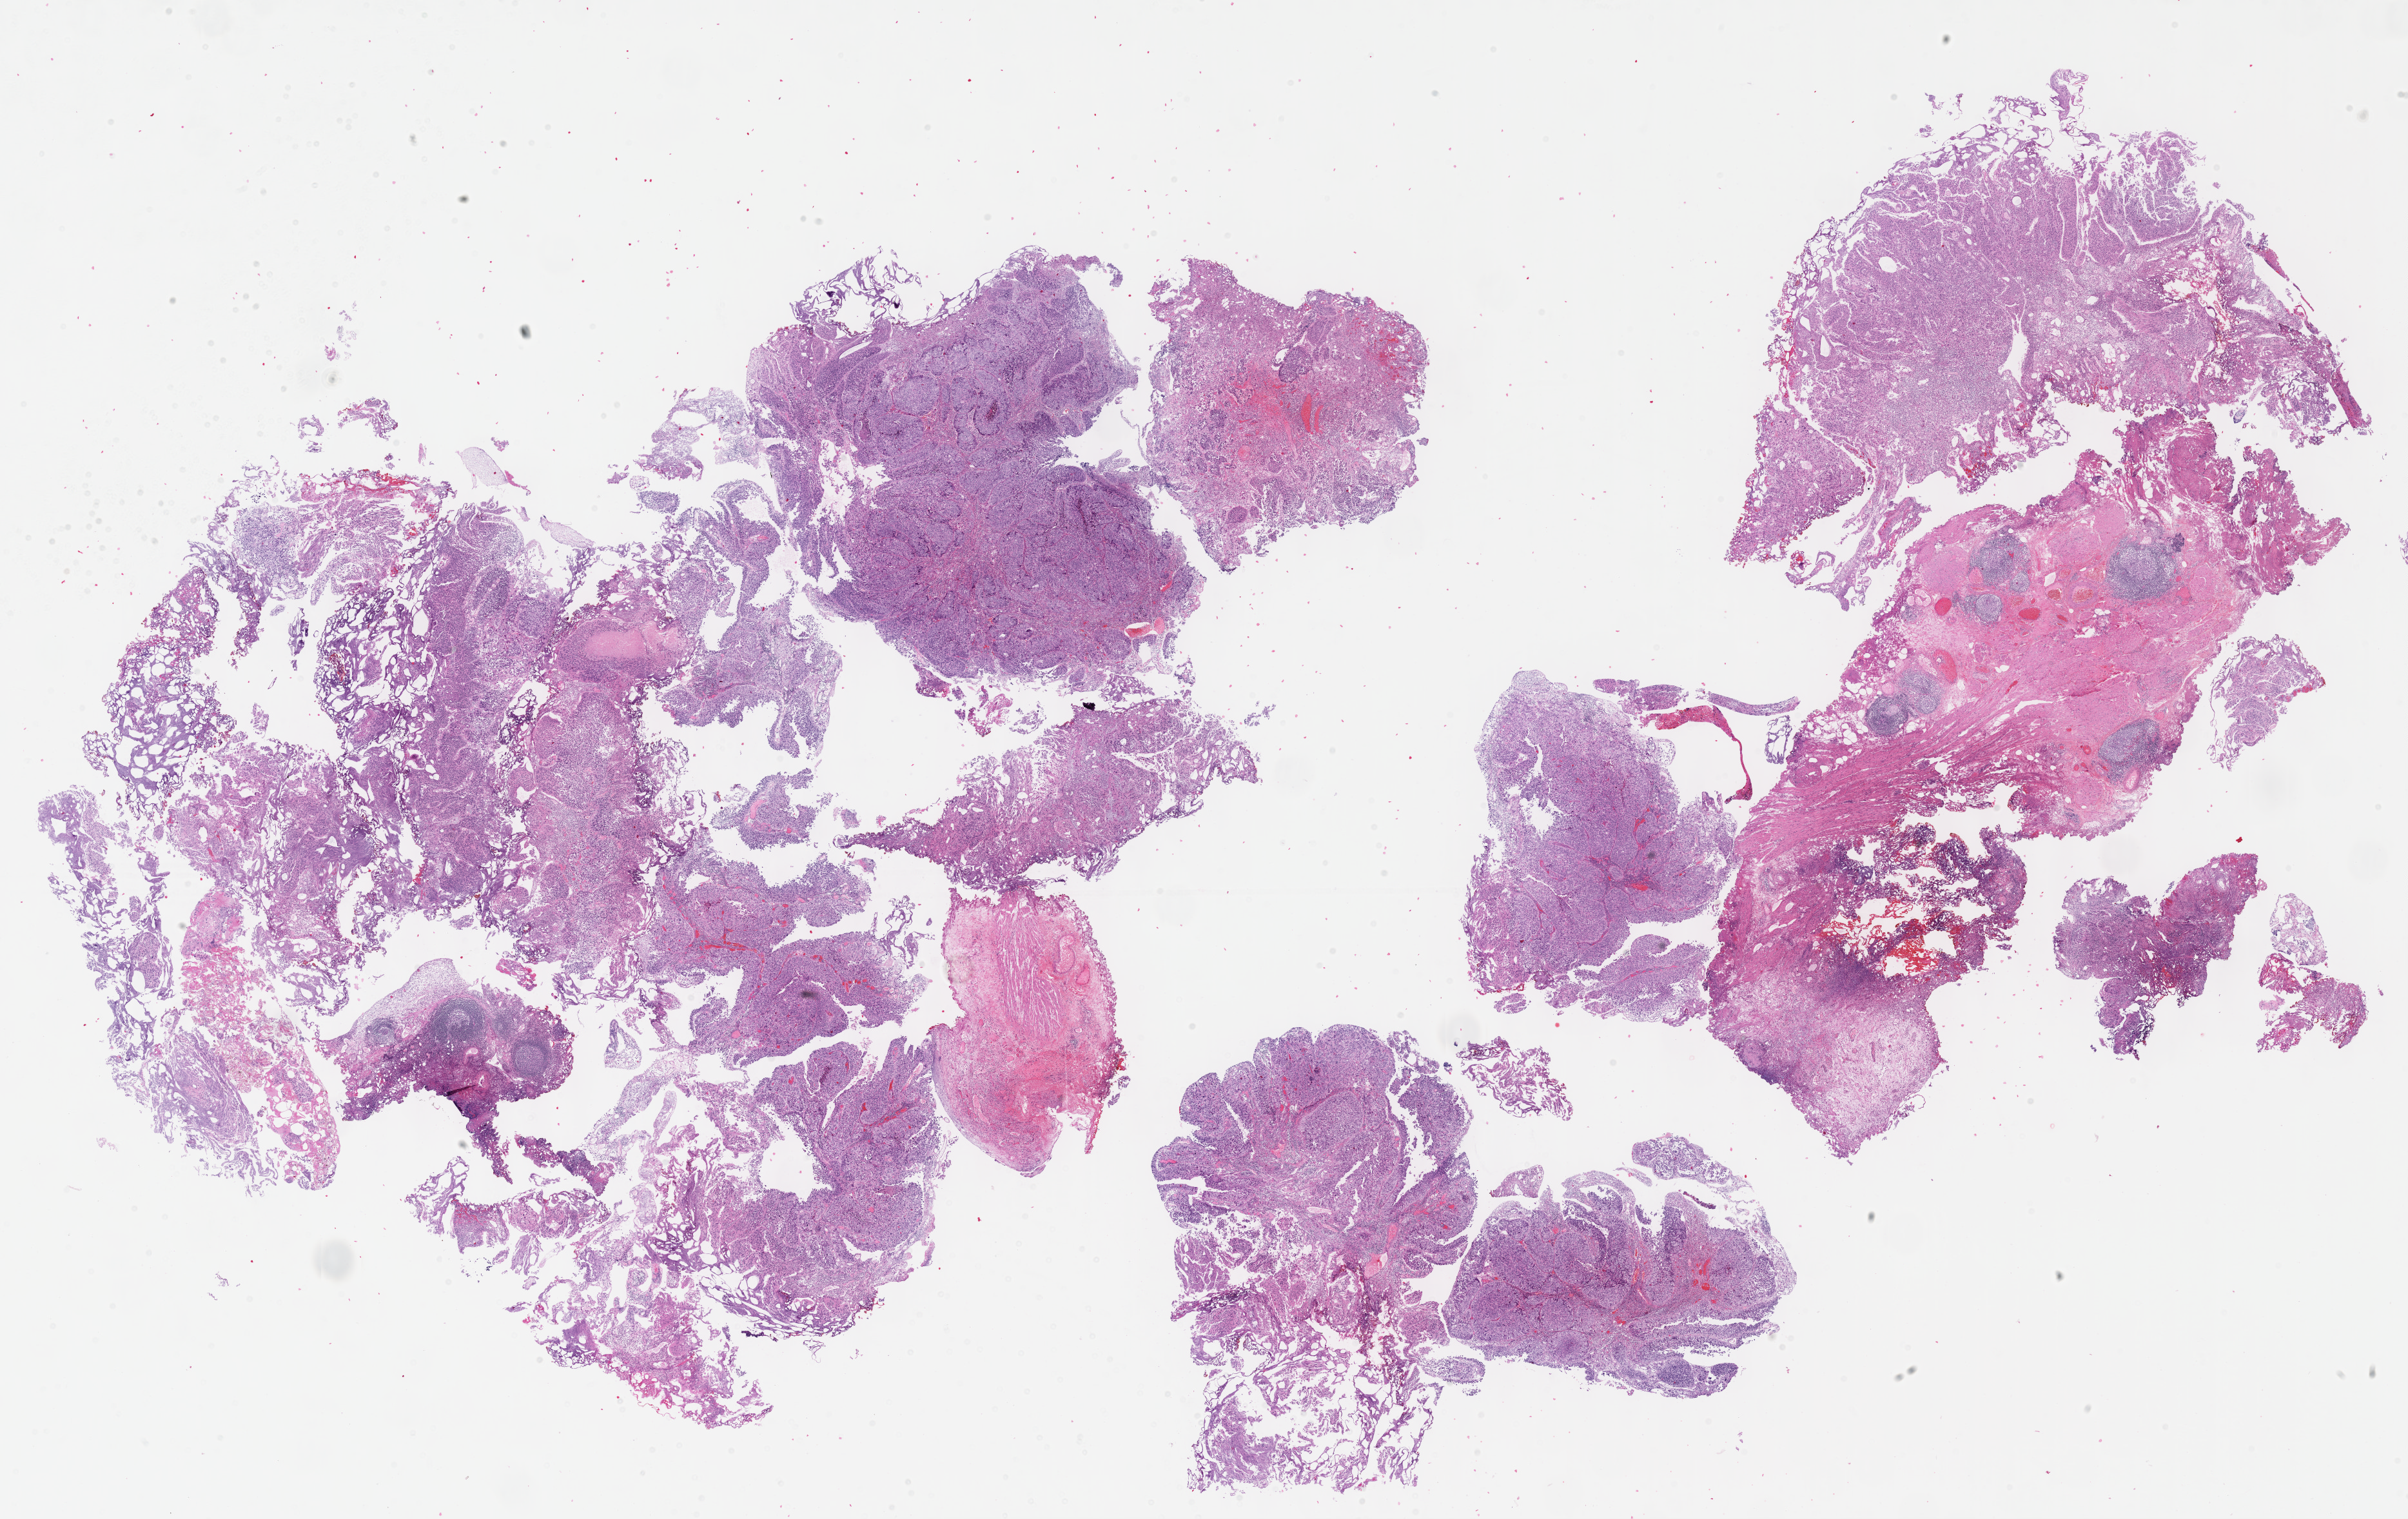
H&E-stained whole-slide image — whole scanned area (about 30.2 x 19.0 mm) shown as a low-resolution overview. FFPE section. Primary tumour sample from the bladder. Patient: female, age at initial diagnosis 75 years. Histologic grade: high grade.
- lymph nodes positive (case pathology): 0 of 25 examined
- AJCC pathologic stage: II (6th edition)
- pathologic diagnosis: Transitional cell carcinoma